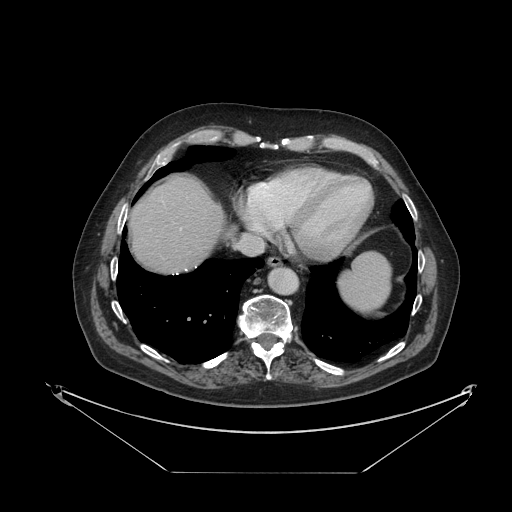
Contrast-enhanced abdominal CT, one axial slice. Position 110 of 121 along the scan axis. Reconstruction kernel STANDARD. 120 kVp. Soft-tissue window (W 400 / L 40 HU). 2.5 mm slice thickness. 512 × 512 image matrix, field of view 500 × 500 mm. Male patient, age 68 years. Case-level facts recorded for this patient, not image findings: diagnosis: colorectal cancer liver metastases, imaged before liver resection; multiple liver metastases: no; largest metastasis: 4 cm; disease in both lobes: no.
Annotated regions visible in this slice (outlined manually by an expert reader):
- liver: box from (x=132, y=177) to (x=225, y=273) px
- planned liver remnant (the part of the liver to remain after resection): (x=131, y=177)–(x=224, y=272)